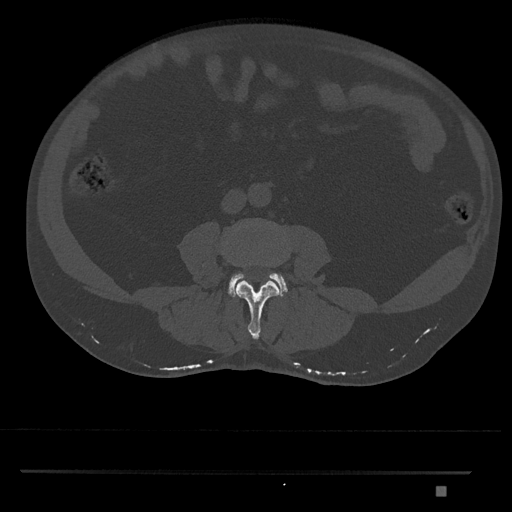
CT including the spine, one axial slice. Slice 656 of 1134 in the series (ordered by position). 120 kVp. Bone window (W 1800 / L 400 HU). 512 × 512 image matrix, field of view 429 × 429 mm. Patient: male, 65 years. From the clinical record (not read from this slice): primary cancer: prostate.
Structures marked on this image (semi-automatic segmentation, software-assisted and operator-edited):
- L3 vertebra: box from (x=222, y=252) to (x=280, y=340) px
- L4 vertebra: (x=228, y=272)–(x=288, y=297)